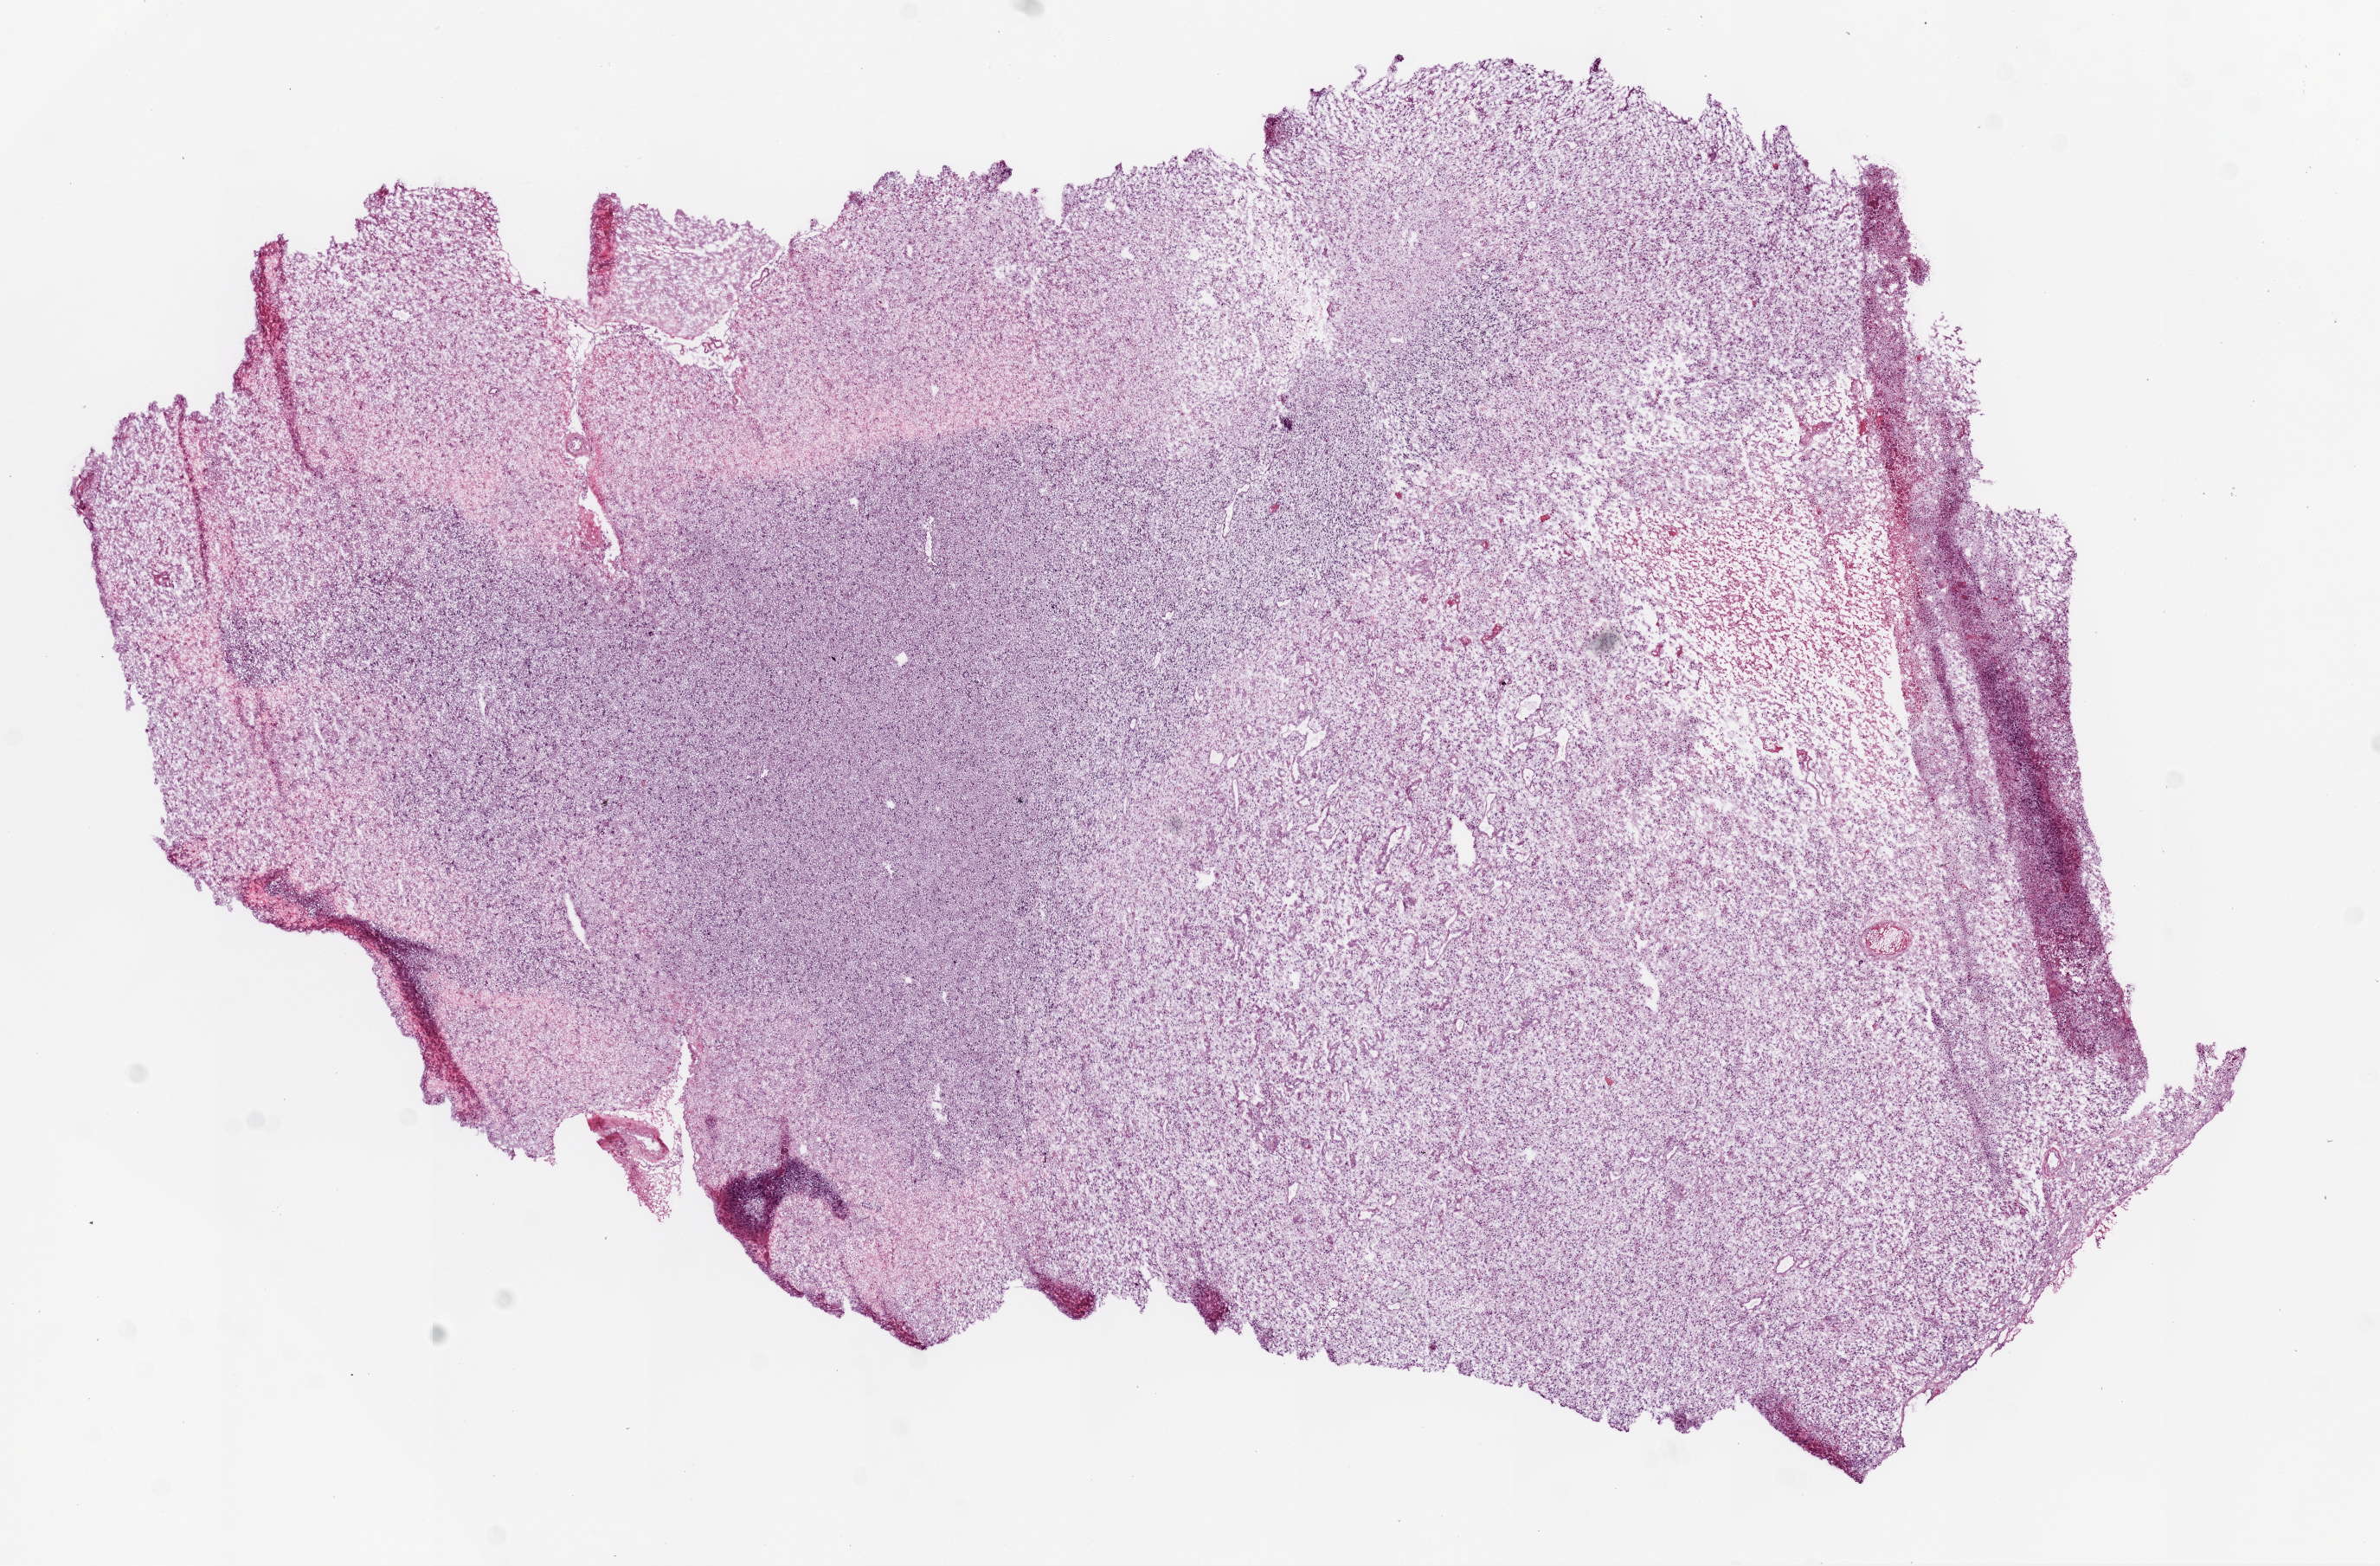
Whole-slide histology image, Hematoxylin and eosin (H&E) stained, low-resolution overview of the scanned area, about 11.0 x 7.3 mm (slide scanned at 20x), frozen section from the bottom of the tissue portion, sample: primary tumour, brain. Patient: female, age at initial diagnosis 64 years. Slide review estimates, as recorded: tumour cells 65%, tumour nuclei 80%, normal cells 10%, stromal cells 5%, necrosis 25%.
Diagnosis: Glioblastoma.